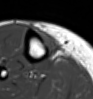
MRI of an extremity soft-tissue mass, one axial slice; MR volume resampled by the dataset authors to the PET/CT grid (not the native acquisition matrix); 3.27 mm slice thickness; 93 × 99 image matrix, field of view 91 × 97 mm. Female patient. From the clinical record (not read from this slice): histological type: undifferentiated – high grade; grade: high; site of the primary tumour: right thigh.
Outlined on this slice (expert contour drawn on MRI and transferred to this co-registered scan by the dataset authors):
- gross tumour volume (mass): box from (x=36, y=29) to (x=60, y=55) px